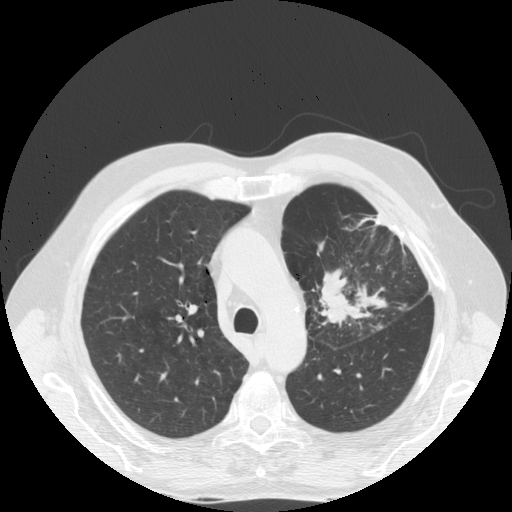
Low-dose screening chest CT, one axial slice. Slice 123 of 170 in the series (ordered by position). Lung window (W 1500 / L -600 HU). 512 × 512 image matrix, field of view 380 × 380 mm.
Outlined on this slice (expert manual segmentation):
- lesion 1 (tumor, upper lobe of left lung): bounding box <319,269,357,325> (left, top, right, bottom; pixels)